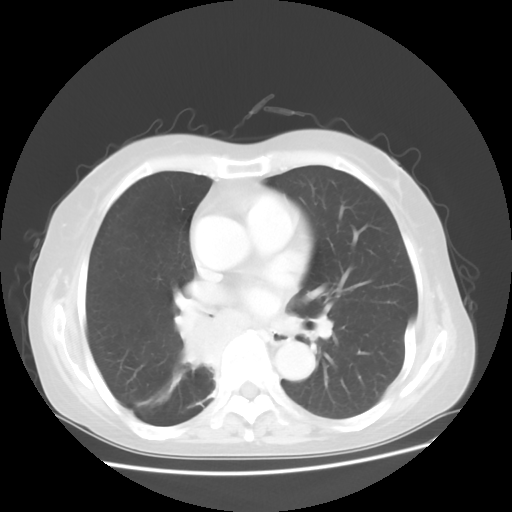
Chest CT, one axial slice; position 24 of 48 along the scan axis; reconstruction kernel STANDARD; lung window (W 1500 / L -600 HU); 512 × 512 image matrix. Female patient, age 63 years. From the clinical record (not read from this slice): clinical TNM (as recorded): T2 N3 M1b.
Structures marked on this image (rectangle marked by the reading radiologist):
- lung tumour (recorded histology: small cell carcinoma): box from (x=175, y=295) to (x=224, y=371) px